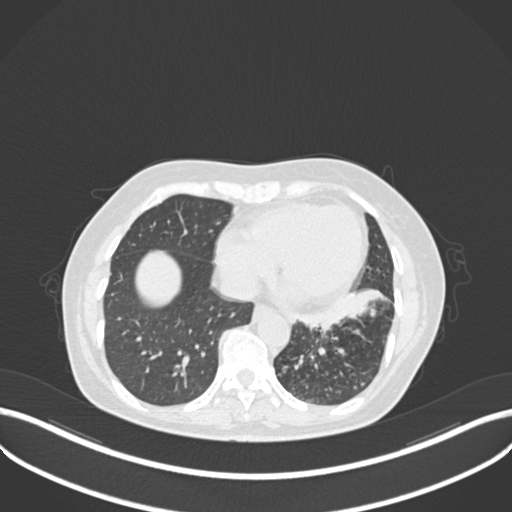
Chest CT, one axial slice. Slice 85 of 270 in the series (ordered by position). Reconstruction kernel B30f. Lung window (W 1500 / L -600 HU). 1 mm slice thickness. 512 × 512 image matrix, field of view 400 × 400 mm. Female patient, age 63 years. Case-level facts recorded for this patient, not image findings: clinical TNM (as recorded): T1b N0 M0; histopathological grade: G2-3.
Annotated regions visible in this slice (rectangle marked by the reading radiologist):
- lung tumour (recorded histology: adenocarcinoma): bounding box <291,283,386,328> (left, top, right, bottom; pixels)